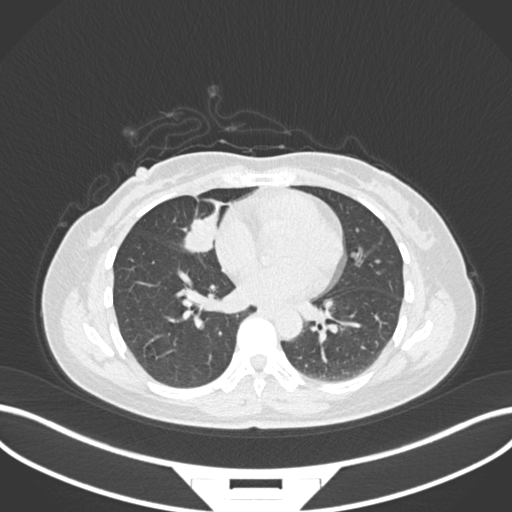
Chest CT, one axial slice; position 68 of 171 along the scan axis; lung window (W 1500 / L -600 HU); 1 mm slice thickness; 512 × 512 image matrix, field of view 400 × 400 mm. Female patient, age 43 years. From the clinical record (not read from this slice): clinical TNM (as recorded): T1c N3 M1.
Outlined on this slice (bounding box drawn by a radiologist):
- lung tumour (recorded histology: adenocarcinoma): bounding box <179,214,219,258> (left, top, right, bottom; pixels)